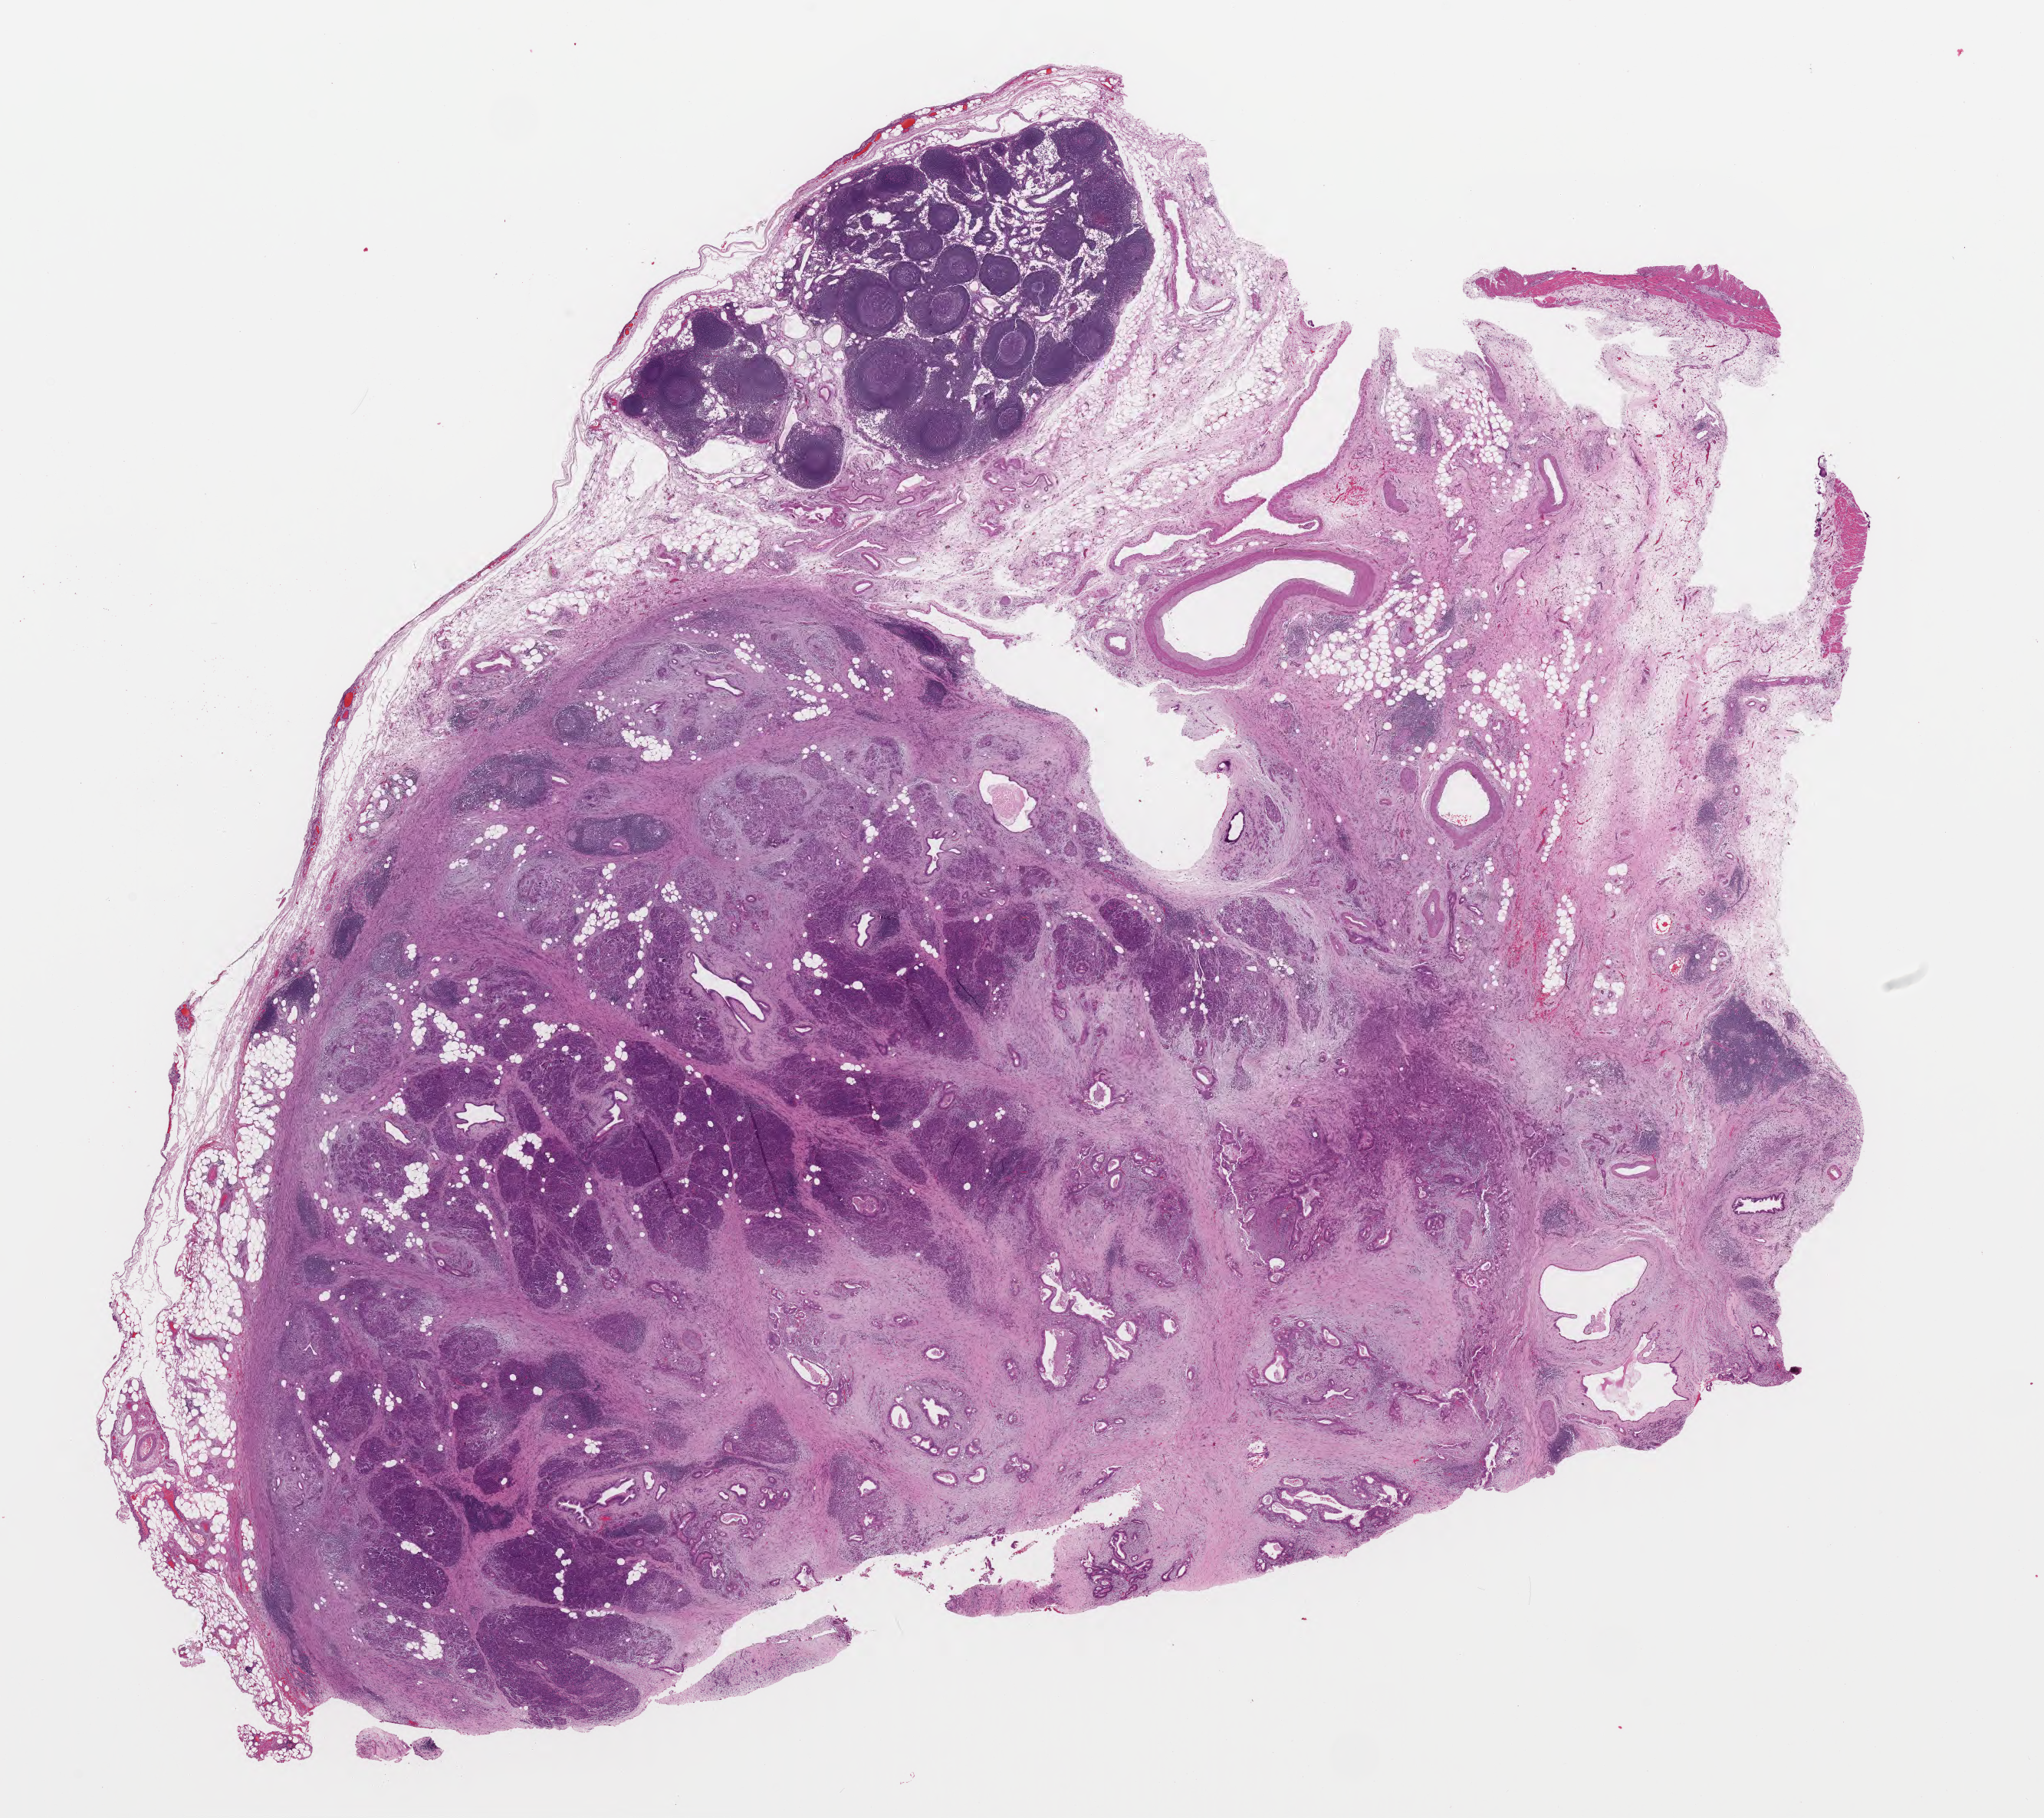
H&E whole-slide image, whole scanned area (about 21.1 x 18.7 mm, from a 40x scan) shown as a low-resolution overview; formalin-fixed paraffin-embedded (FFPE) diagnostic section; sample: primary tumour, pancreas. Female, age 81 years at initial diagnosis. Histologic grade: G2 (moderately differentiated).
Histologic diagnosis: Infiltrating duct carcinoma, NOS (head of pancreas). AJCC pathologic stage: IIB (7th edition). Lymph nodes positive (case pathology): 4 of 20 examined.